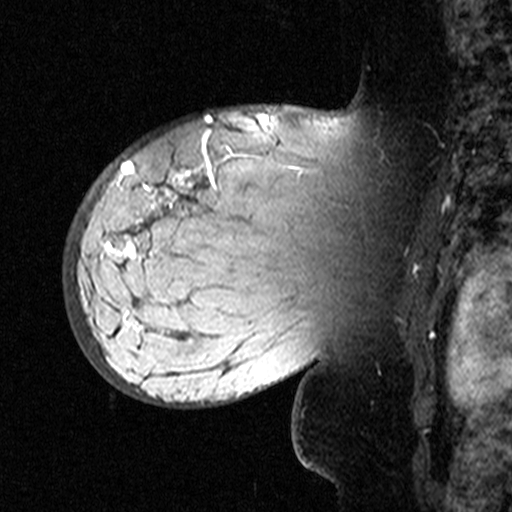
Breast MRI (dynamic contrast-enhanced), one sagittal slice. Slice 32 of 44 in the series (ordered by position). Dynamic contrast-enhanced study with each time point stored as its own series, time point 2 of 3 at this slice position (early post-contrast, ordered by acquisition time). 1.5 T. TE 4.5 ms, TR 11 ms. 512 × 512 image matrix. Female patient, age 53 years. From the clinical record (not read from this slice): setting: breast cancer imaged before/during neoadjuvant chemotherapy; receptor status: HR-positive, HER2-negative.
Annotated regions visible in this slice (semi-automatic segmentation, software-assisted and operator-edited):
- analysis volume of interest (the breast-tissue region the enhancement analysis was run in; not a lesion): bounding box <76,140,311,353> (left, top, right, bottom; pixels)
- tumour enhancement mask (voxels above the 90 % enhancement threshold inside the analysis volume of interest): <108,149,216,260>